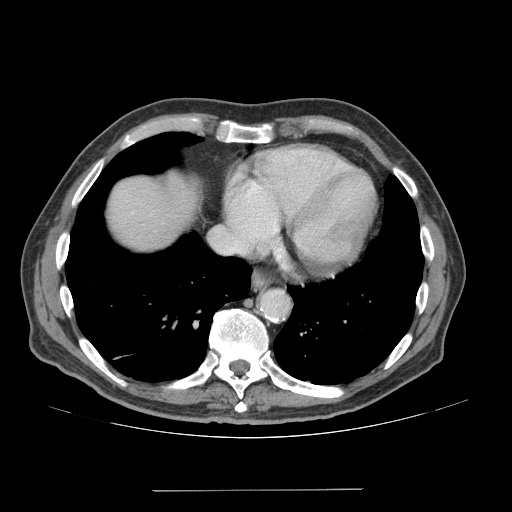
Contrast-enhanced abdominal CT (liver protocol), one axial slice. Position 67 of 77 along the scan axis. Reconstruction kernel STANDARD. 140 kVp. Soft-tissue window (W 400 / L 40 HU). 2.5 mm slice thickness. 512 × 512 image matrix, field of view 400 × 400 mm. Case-level facts recorded for this patient, not image findings: diagnosis: hepatocellular carcinoma (patient treated with transarterial chemoembolisation; whether this scan precedes or follows treatment is not stated here); TNM stage (as recorded): Stage-IVA; Child-Pugh class: A; tumour differentiation: well differentiated.
Annotated regions visible in this slice (semi-automatically segmented with operator editing):
- liver parenchyma outside the tumour (the mass and vessels are separate outlines, so this box may not span the whole liver): bounding box [x1, y1, x2, y2] px = [109, 176, 196, 250]